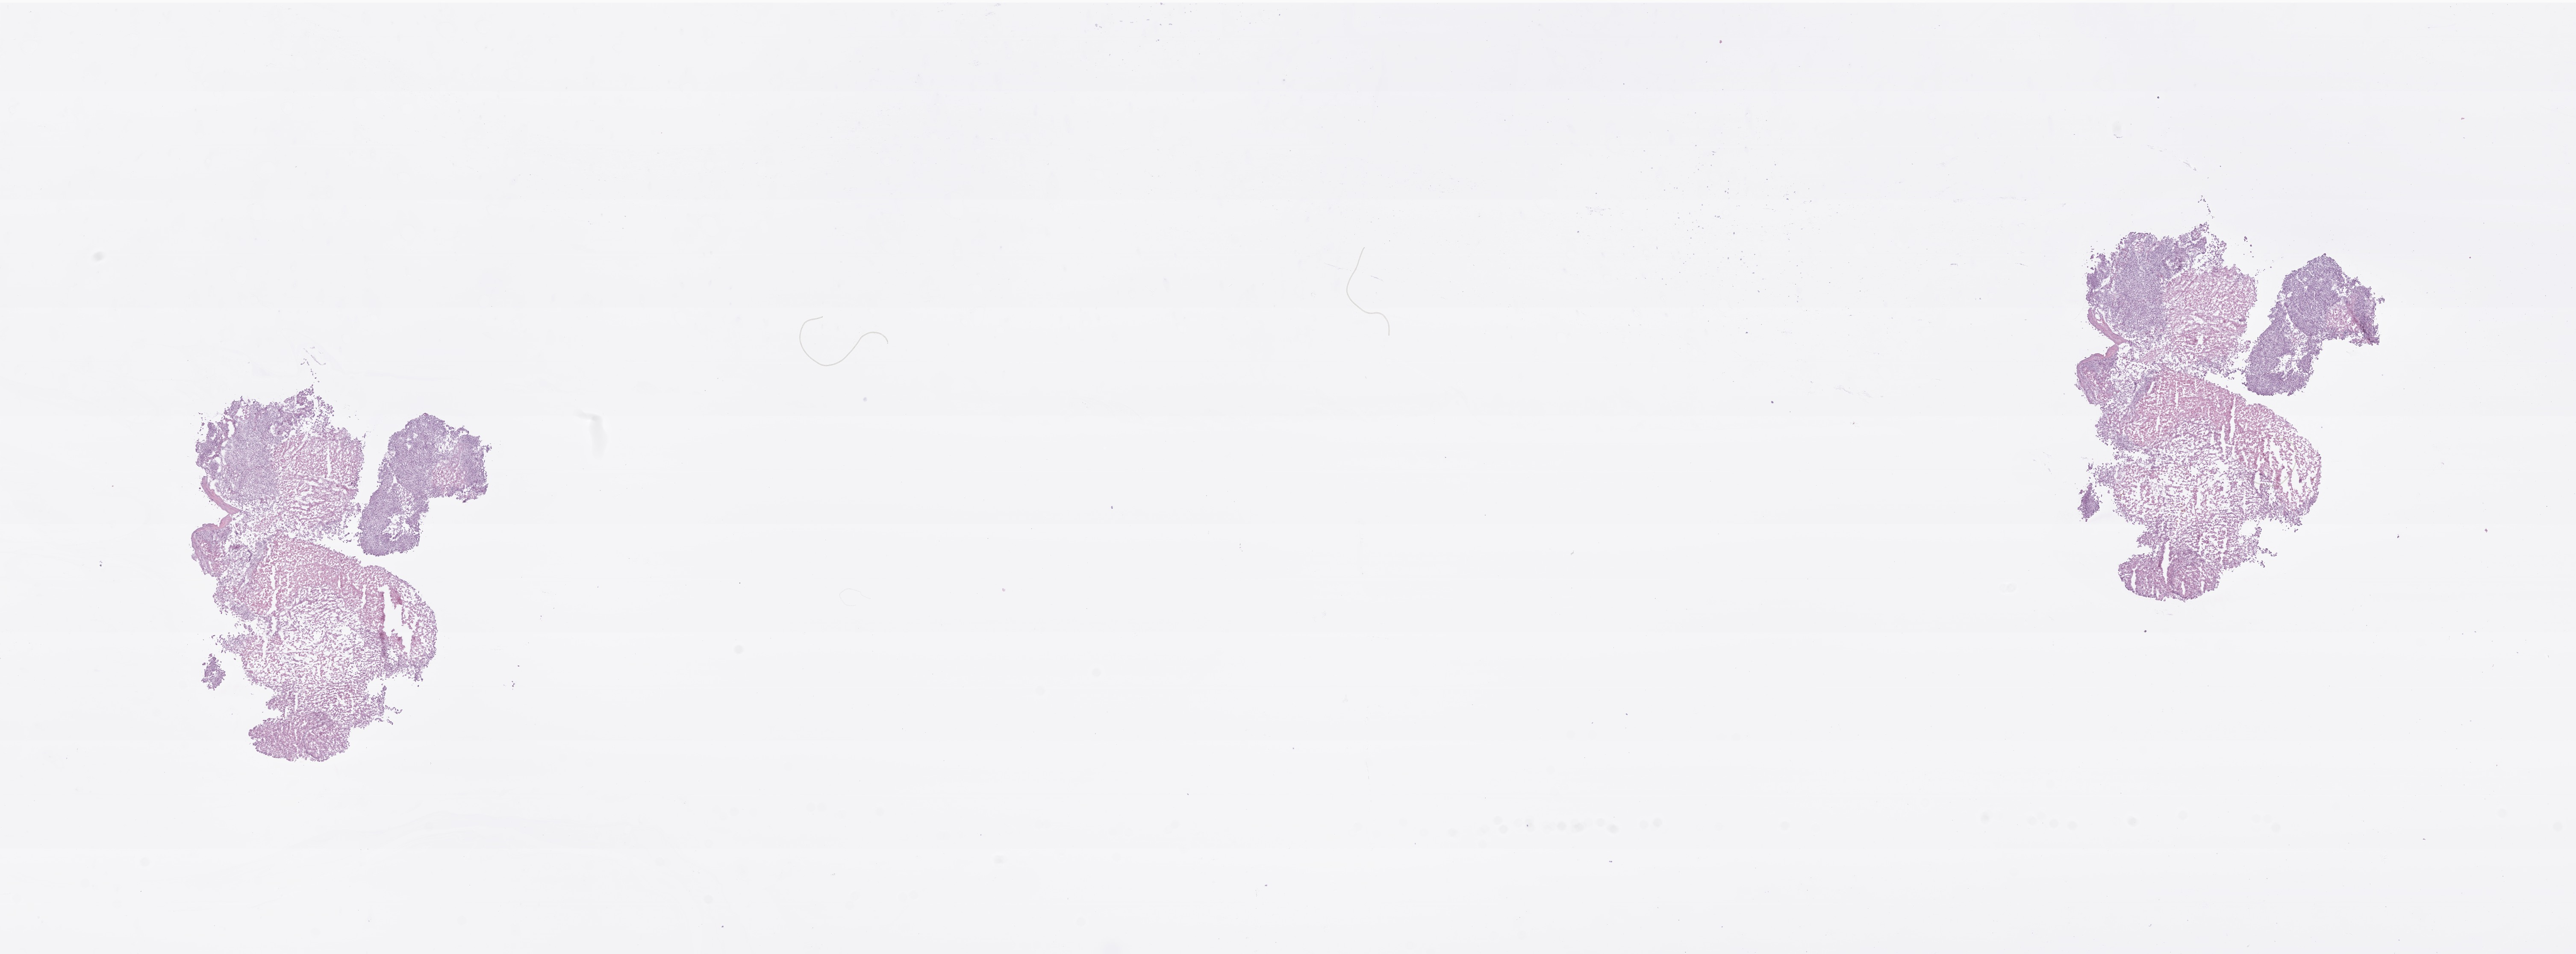
Whole-slide image, hematoxylin and eosin (H&E) stain of tumor tissue from the adrenal gland — low-resolution overview of the scanned area, about 25.3 x 9.4 mm, cryosection (OCT / tissue freezing medium). Patient female; age 183 months (15 years 3 months).
* diagnosis: Adrenal cortical carcinoma